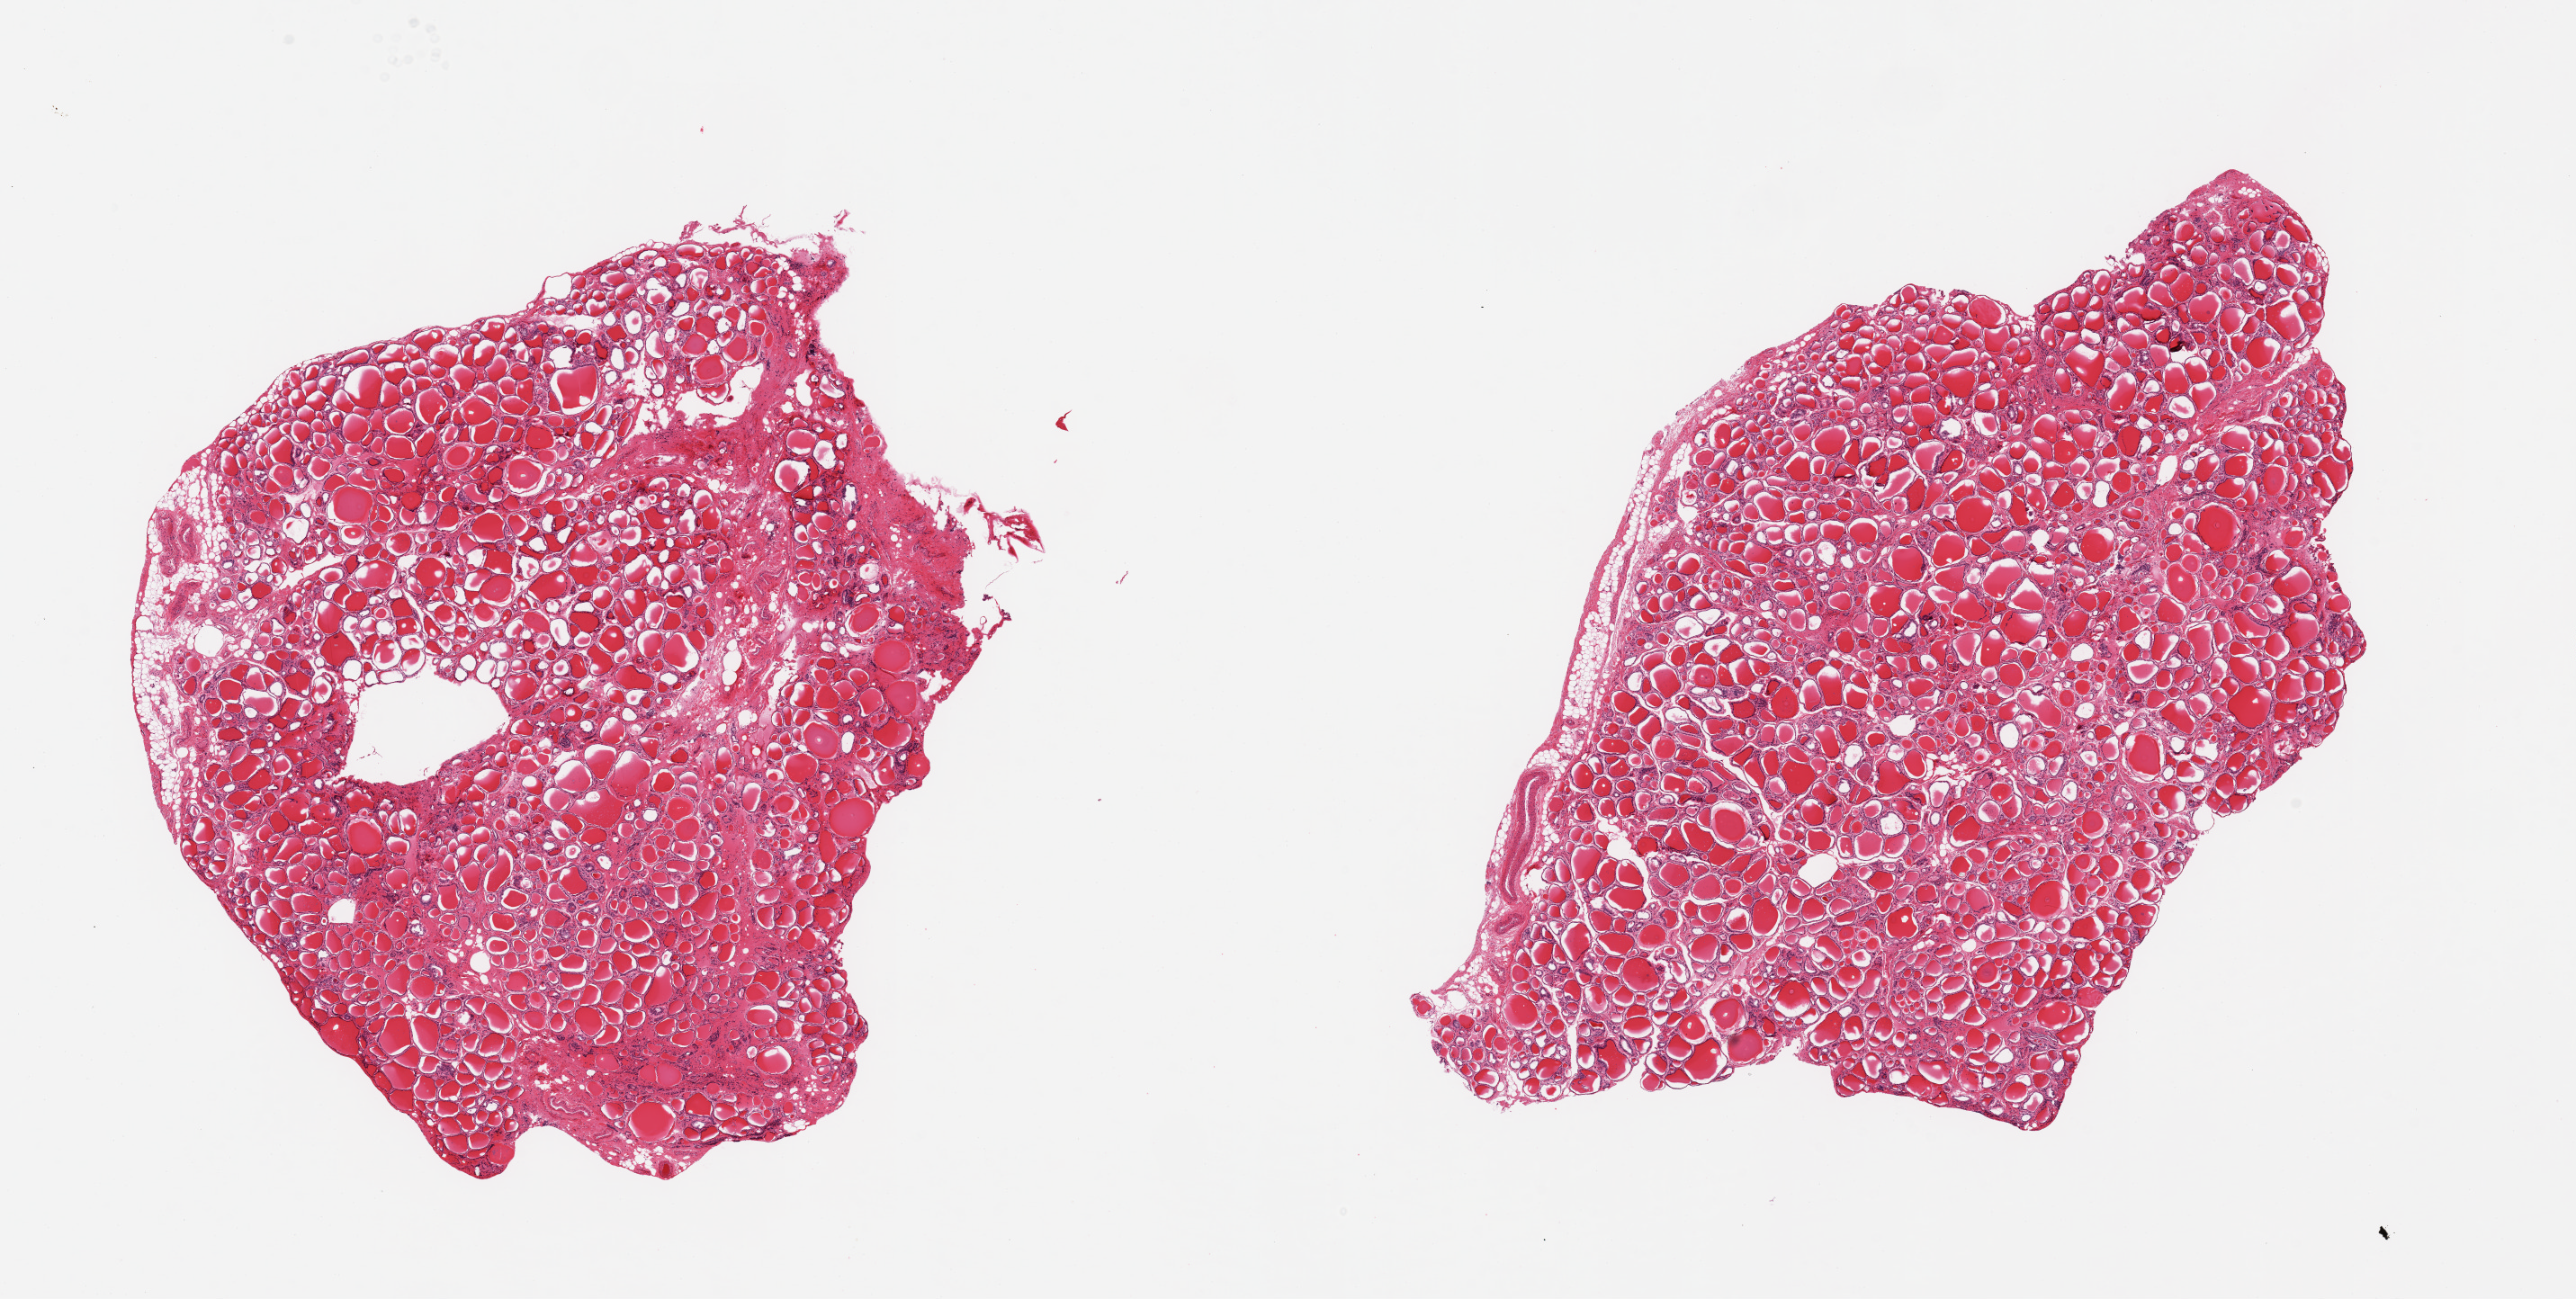
Whole-slide image, H&E stain, brightfield — shown as a low-resolution overview of the whole scanned area (about 22.6 x 11.4 mm). PAXgene-fixed, paraffin-embedded tissue. Target tissue: thyroid. Tissue donor sample. Donor: male.
* review note (as recorded): 2 pieces, no abnormalities